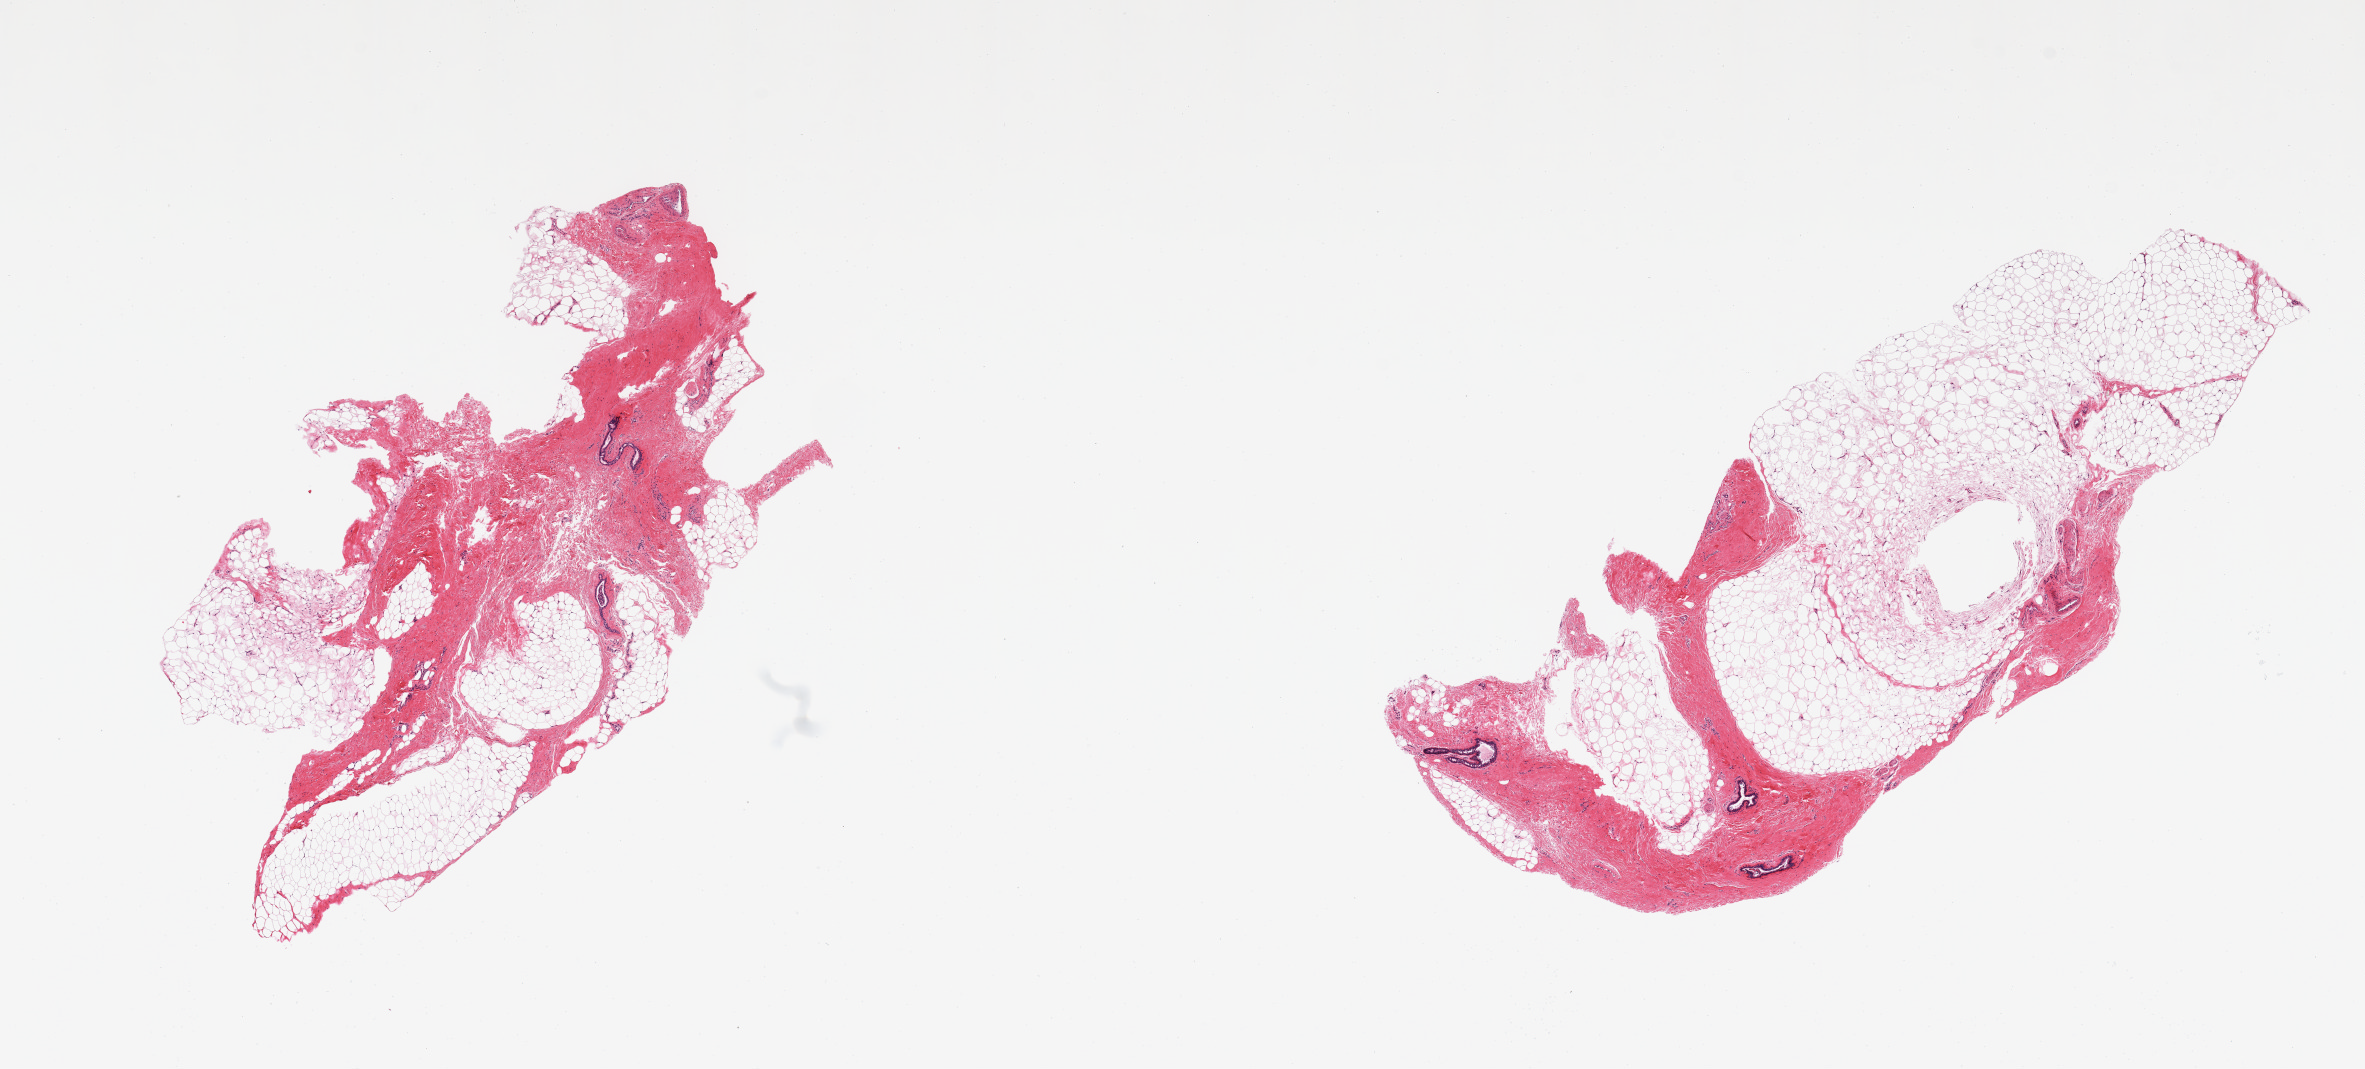
Whole-slide image, haematoxylin and eosin stain, low-resolution overview of the scanned area, about 18.7 x 8.5 mm; PAXgene-fixed paraffin-embedded (PFPE) section; sampled site (target tissue): breast; donor tissue sample. Donor: male.
- reviewer comment on this tissue sample: 2 pieces; fibrofatty tissue with several mammary ducts